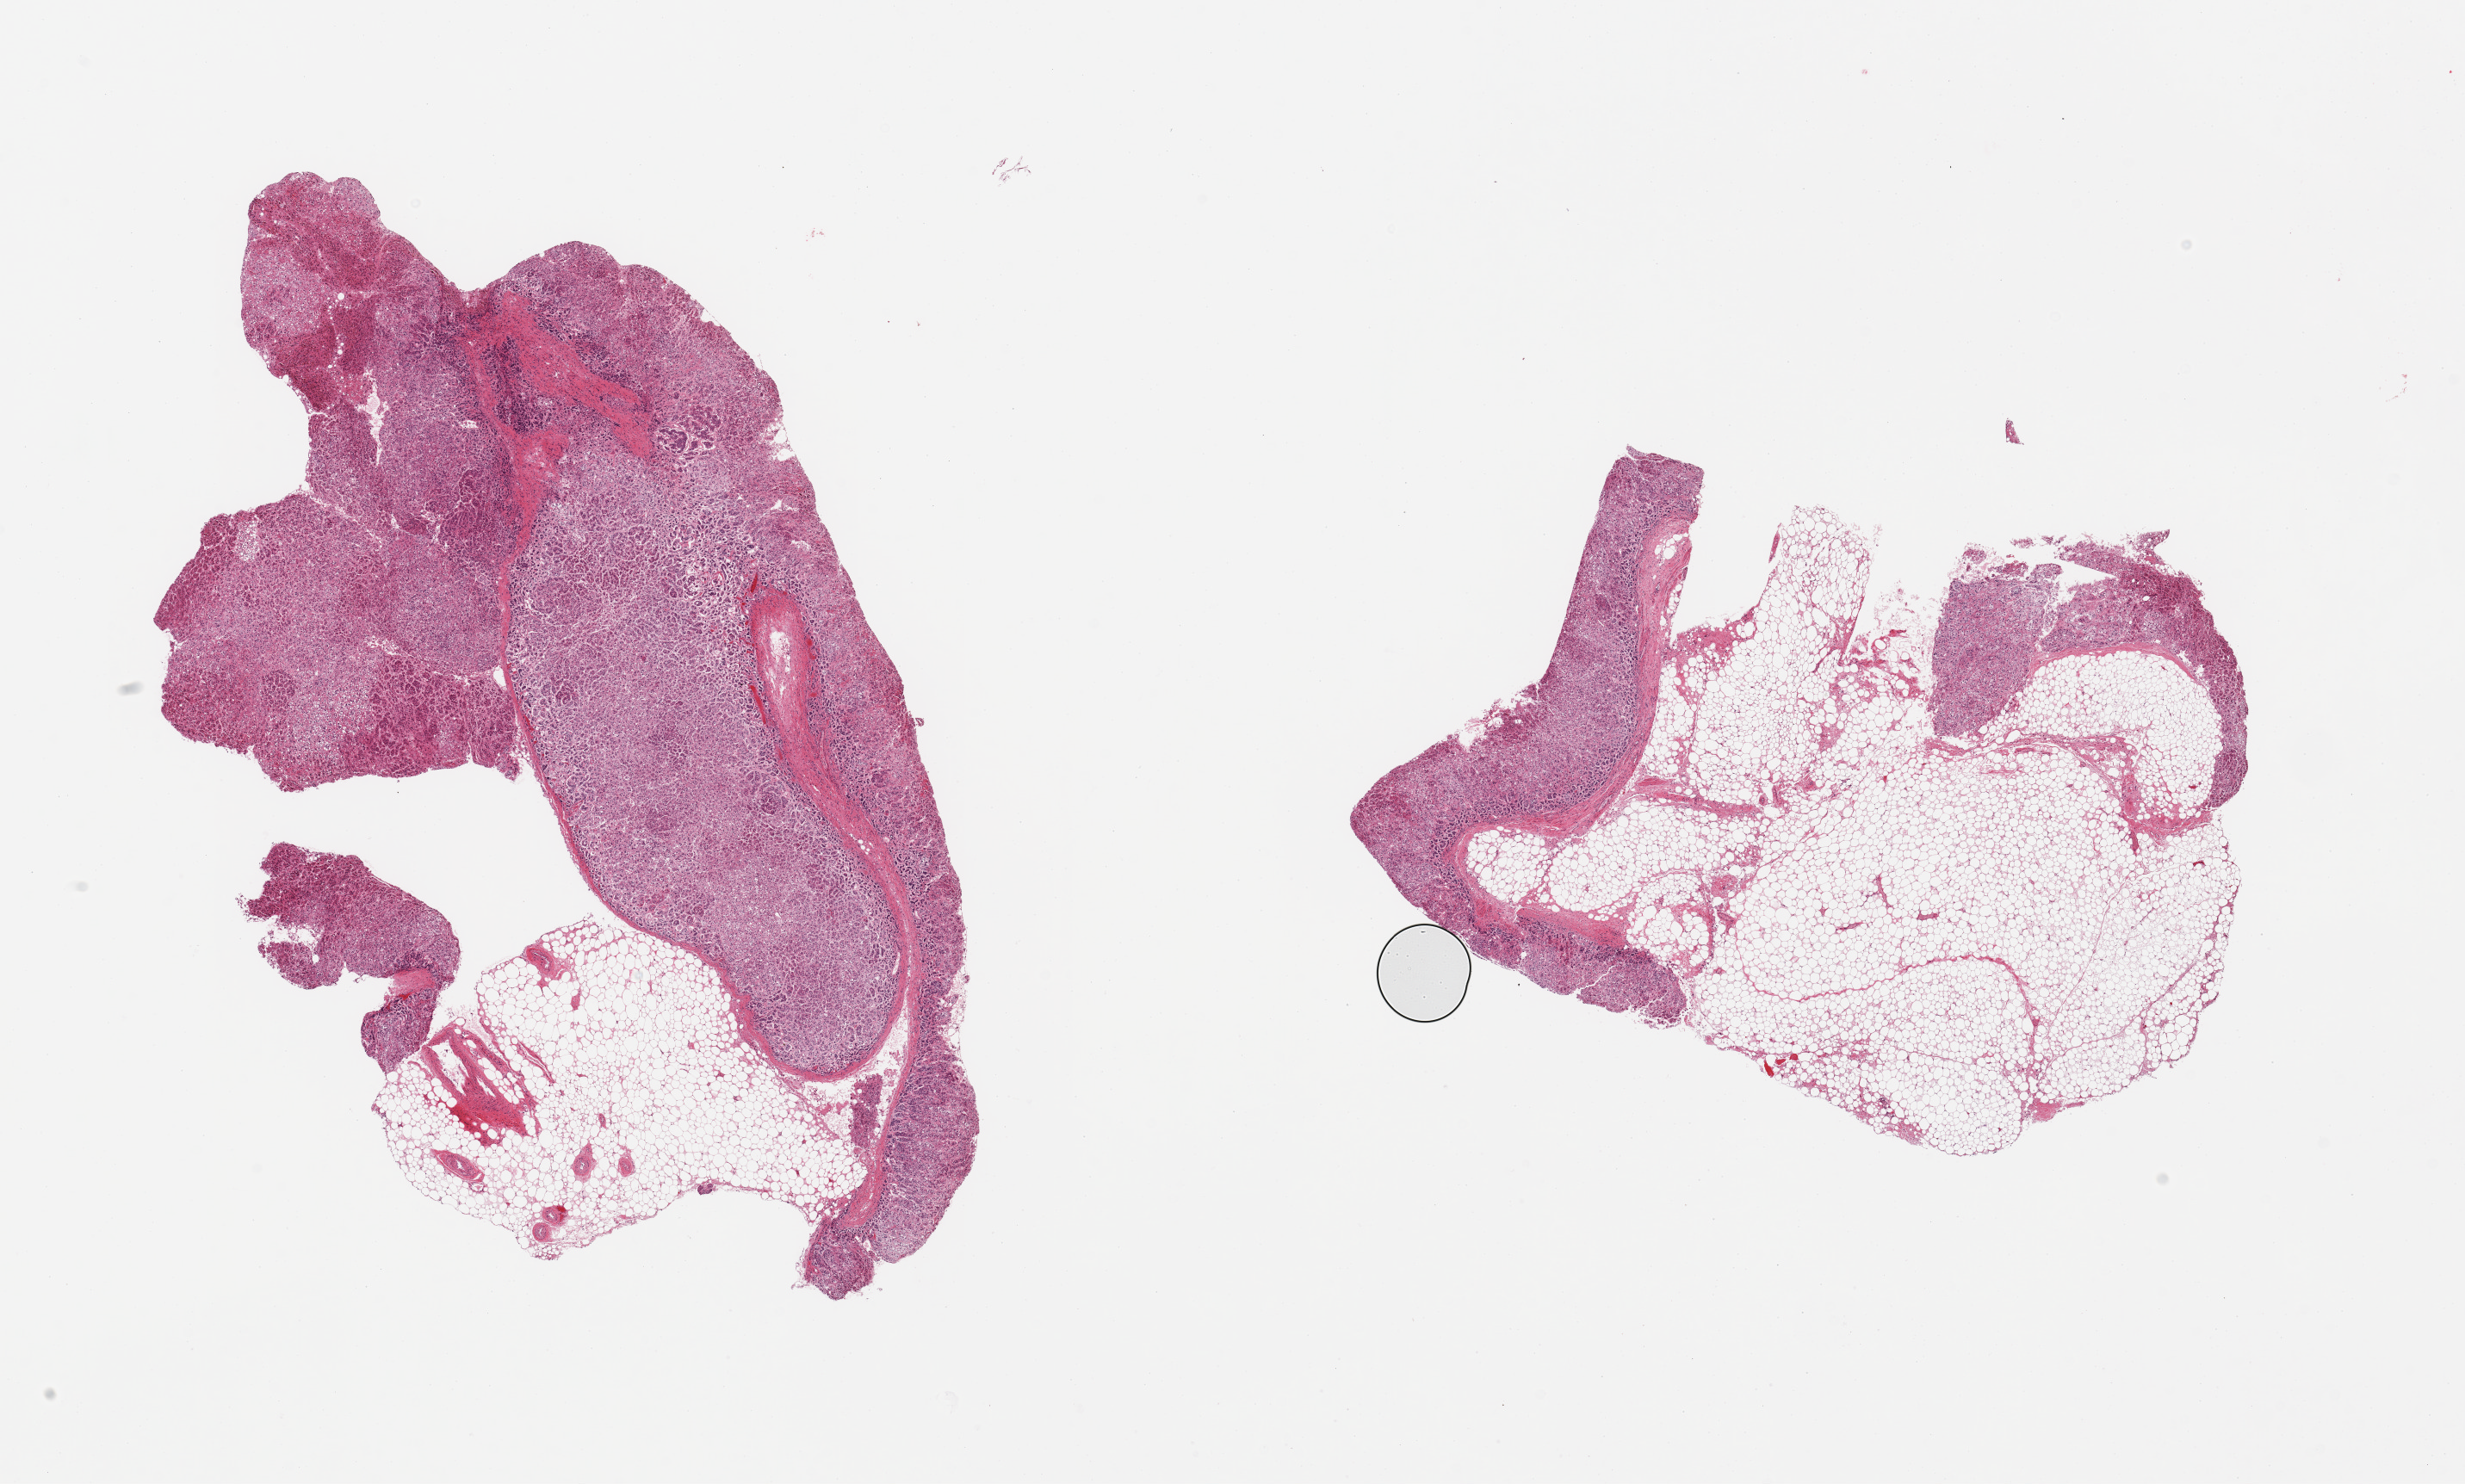
Digitized haematoxylin and eosin-stained section, shown as a low-resolution overview of the whole scanned area (about 22.6 x 13.6 mm). PAXgene-fixed paraffin-embedded (PFPE) section. Sampled site (target tissue): adrenal gland. Tissue donor sample. Donor sex: female.
Reviewer comment on this tissue sample: 2 pieces; 80% & 20% fat.